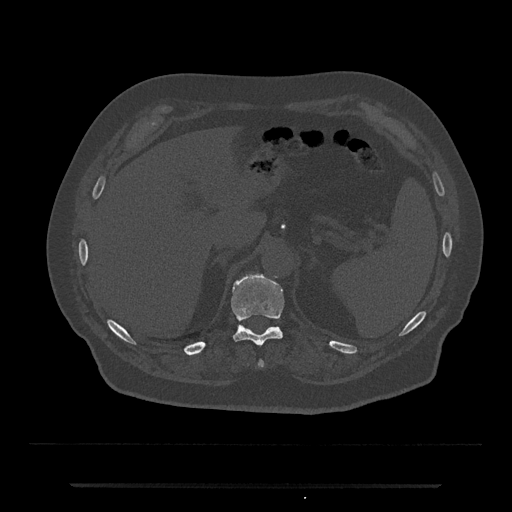
CT including the spine, one axial slice; slice 648 of 797 in the series (ordered by position); reconstruction kernel Br40s/3; bone window (W 1800 / L 400 HU); 0.5 mm slice thickness; 512 × 512 image matrix. Male patient, age 80 years. From the clinical record (not read from this slice): primary cancer: prostate; vertebrae with lytic lesions (as recorded): L1, T11.
Outlined on this slice (semi-automatically segmented with operator editing):
- T10 vertebra: box from (x=260, y=361) to (x=264, y=366) px
- T11 vertebra: (x=230, y=275)–(x=285, y=346)